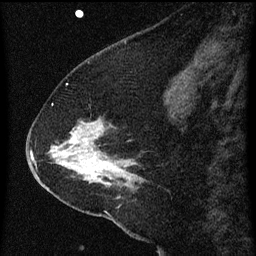
Breast MRI (dynamic contrast-enhanced), one sagittal slice; position 22 of 60 along the scan axis; dynamic contrast-enhanced series, image 2 of 3 at this slice position (ordered by acquisition); 1.5 T; TE 4.2 ms, TR 8 ms; 2 mm slice thickness; 256 × 256 image matrix, field of view 180 × 180 mm. Female patient, age 47 years.
Outlined on this slice (semi-automatic segmentation, software-assisted and operator-edited):
- analysis volume of interest (the breast-tissue region the enhancement analysis was run in; not a lesion): bounding box [x1, y1, x2, y2] px = [36, 102, 149, 213]
- tumour enhancement mask (voxels above the 70 % enhancement threshold inside the analysis volume of interest): [49, 122, 131, 187]